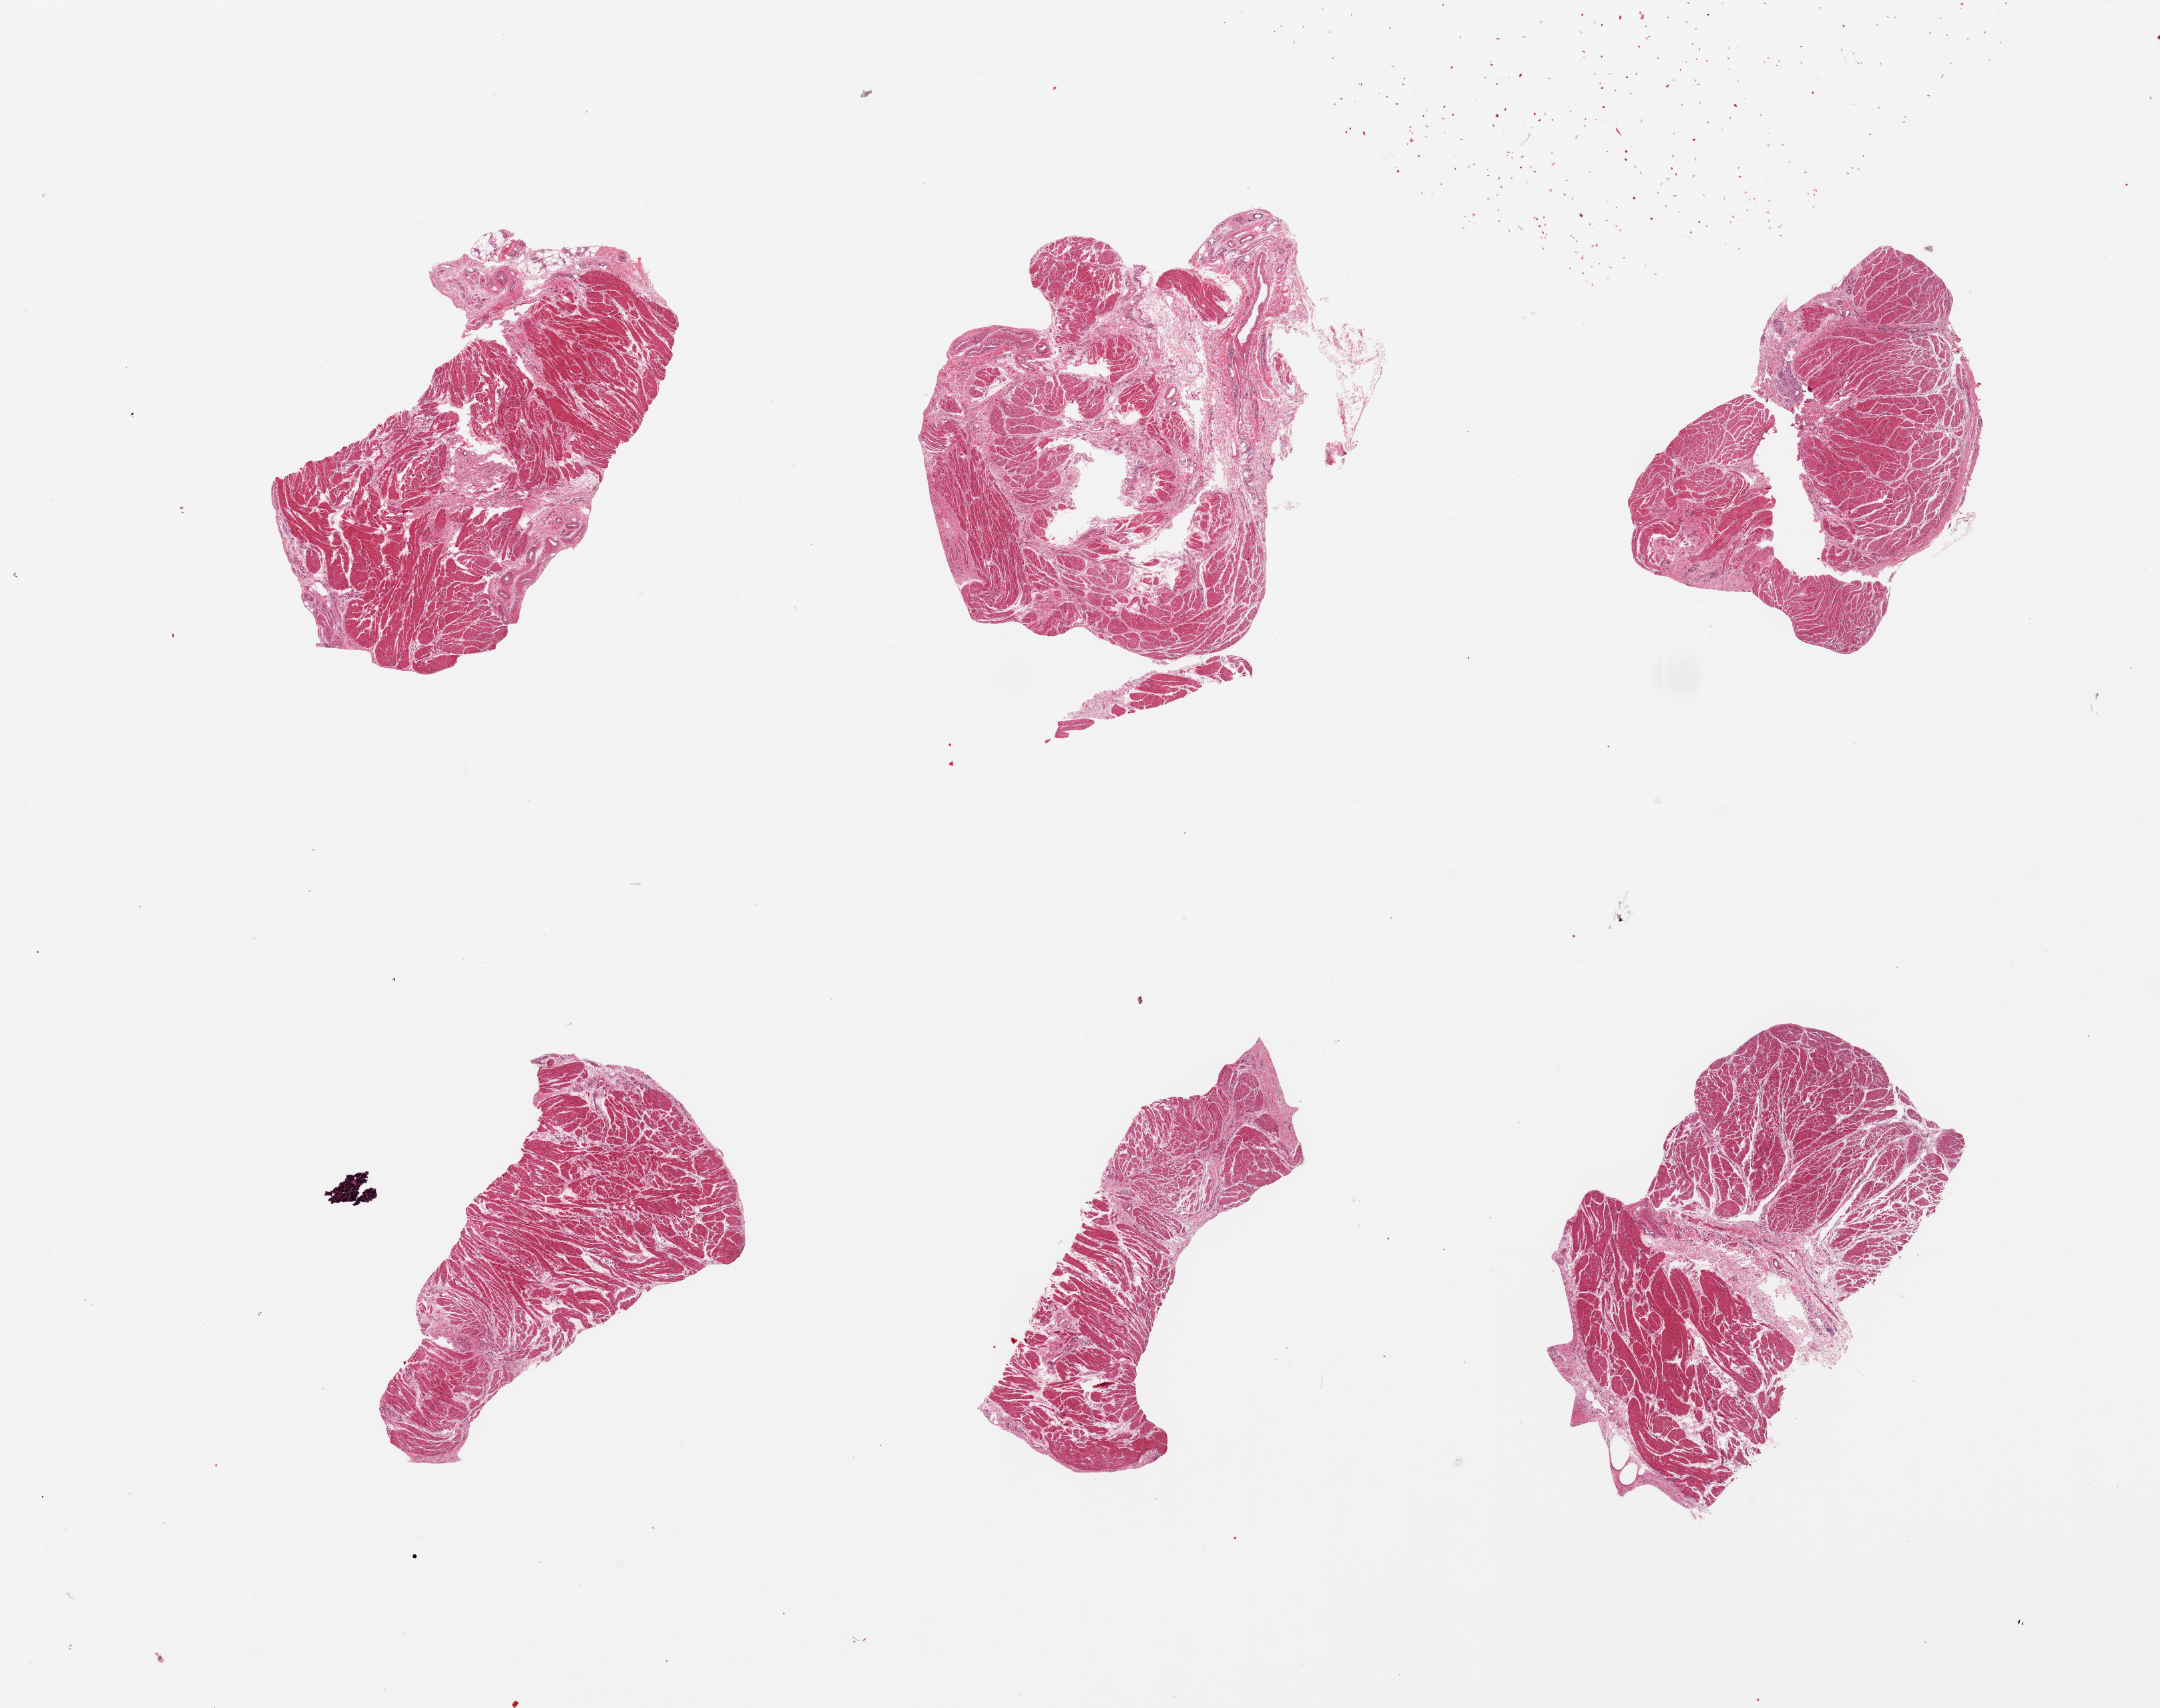
Whole-slide image, H&E stain, low-resolution overview of the scanned area, about 25.6 x 20.2 mm. PAXgene-fixed paraffin-embedded (PFPE) section. Target tissue: esophageal muscle. Tissue donor sample.
- reviewer comment on this tissue sample: 6 pieces, all muscularis, good specimens